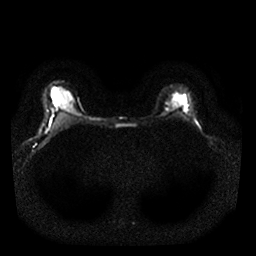
Breast MRI, one axial slice. Diffusion-weighted series; image 2 of 4 stored at this slice position (different b-values; order by instance number). 1.5 T. 4 mm slice thickness. 256 × 256 image matrix, field of view 320 × 320 mm. Female patient.
Structures marked on this image (expert manual segmentation):
- tumour on diffusion-weighted imaging: bounding box (x1, y1, x2, y2) in pixels: (166, 108, 170, 111)